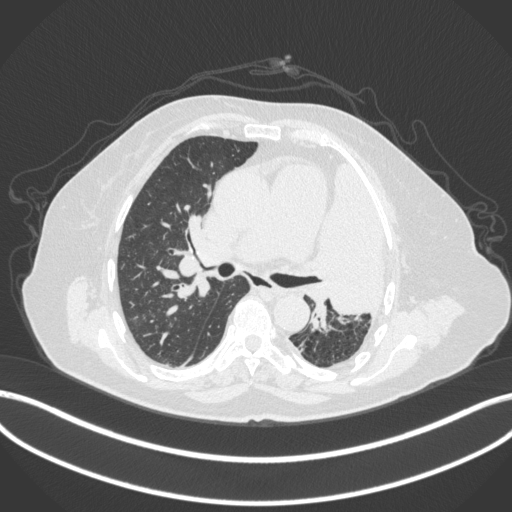
Chest CT, one axial slice. Slice 233 of 399 in the series (ordered by position). 120 kVp. Lung window (W 1500 / L -600 HU). 1 mm slice thickness. 512 × 512 image matrix, field of view 400 × 400 mm. Patient: female, 75 years. From the clinical record (not read from this slice): clinical TNM (as recorded): T3 N3 M1.
Annotated regions visible in this slice (rectangle marked by the reading radiologist):
- lung tumour (recorded histology: adenocarcinoma): bounding box <317,148,389,321> (left, top, right, bottom; pixels)